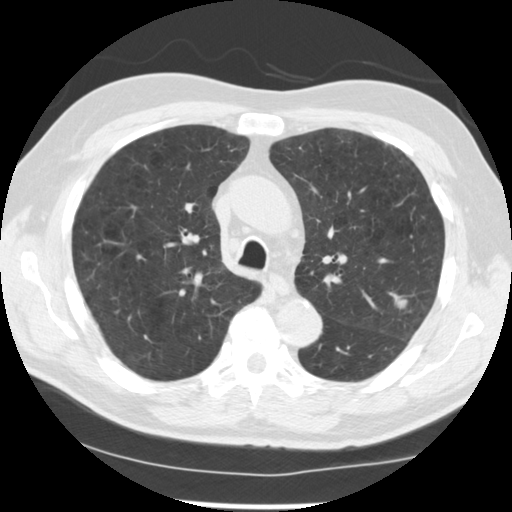
Low-dose screening chest CT, axial slice; baseline screening round; lung window (W 1500 / L -600 HU); 2.5 mm slice thickness; slice 168 of 249 in the series. Male participant, aged 71 years at enrolment. Current smoker at enrolment.
Expert reader's lesion annotation, box from (x=383, y=282) to (x=424, y=327) px. The screening reader recorded 2 non-calcified nodules or masses ≥4 mm on this exam (left upper lobe, left upper lobe); which of them this box marks is not recorded. Official screen result: positive, change unspecified: nodule(s) >= 4 mm or enlarging nodule(s), mass(es), or other non-specific abnormalities suspicious for lung cancer. Later outcome: lung cancer diagnosed 37 days after this screen — adenocarcinoma, NOS, left upper lobe, poorly differentiated (G3), stage IIIB (AJCC 6th edition), 25 mm at pathology.